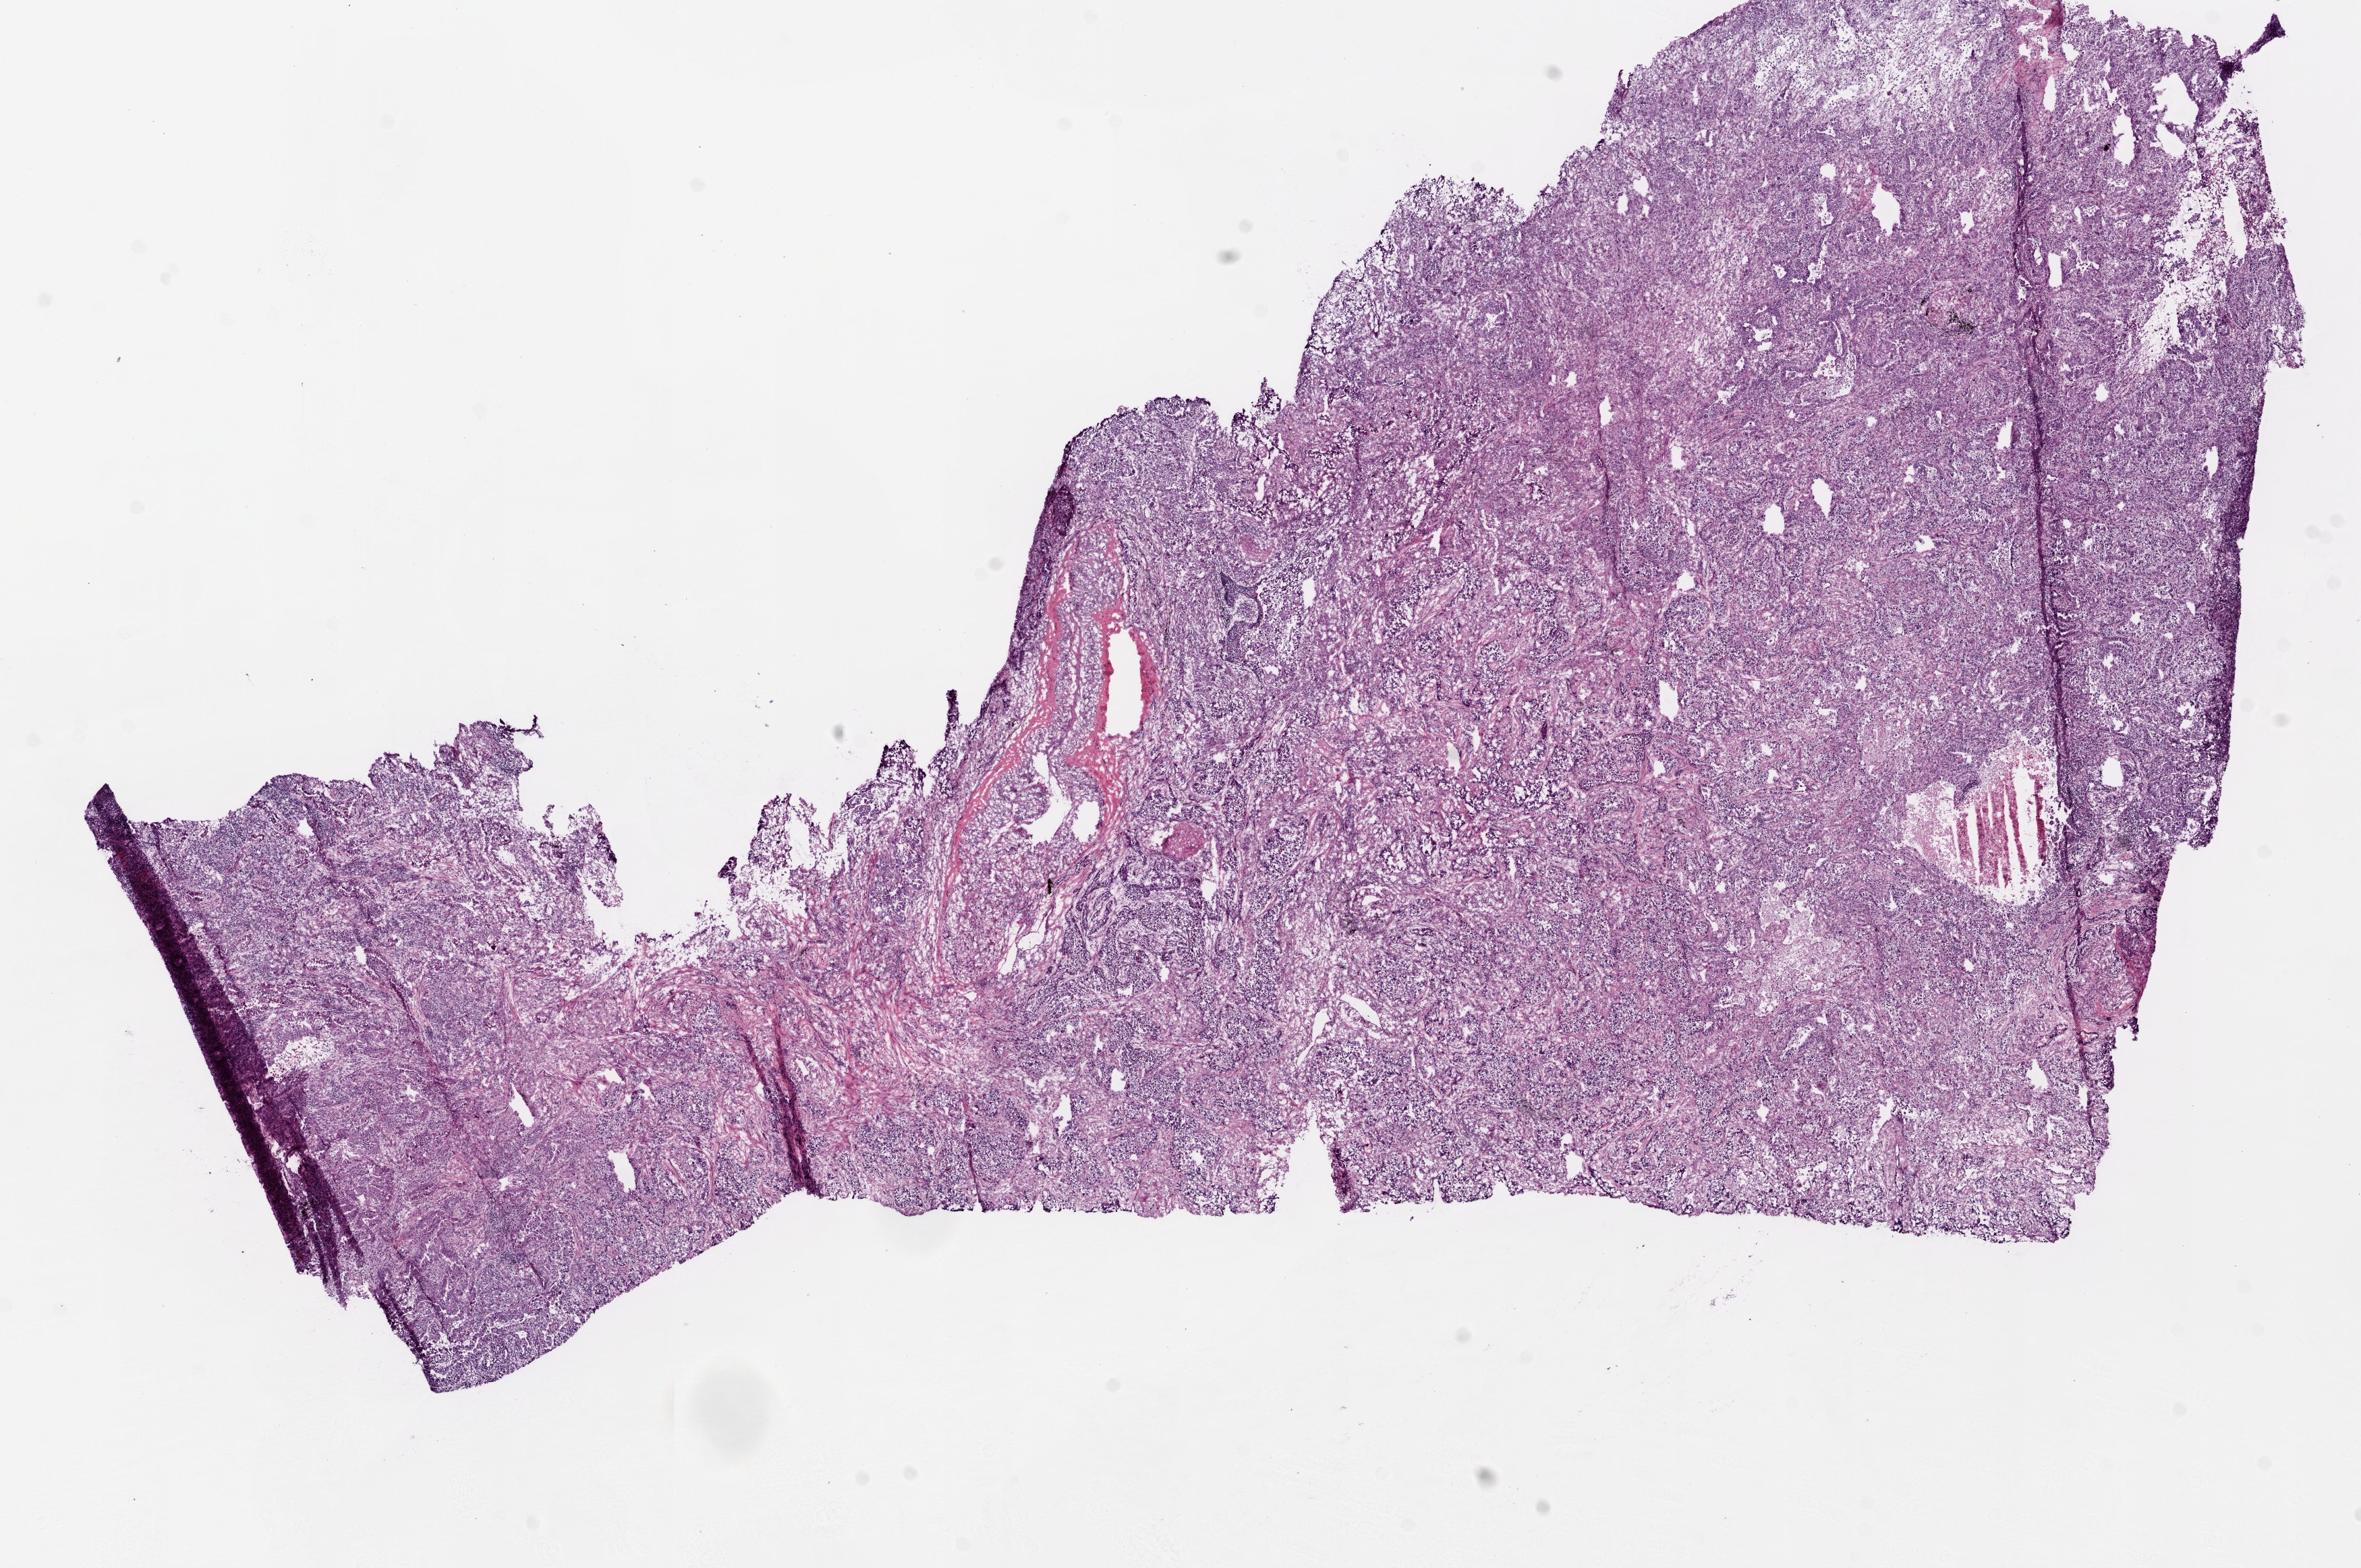
Whole-slide histology image, H&E, shown as a low-resolution overview of the whole scanned area (about 14.0 x 9.3 mm). Frozen section. Primary tumour sample from the lung. Female patient; age at initial diagnosis 56 years. Composition of this section per pathologist review: tumour nuclei 70%, normal cells 3%, stromal cells 15%, necrosis 5%.
Laterality: right. TNM: T2 NX M1. Histologic diagnosis: Adenocarcinoma with mixed subtypes (lower lobe, lung). AJCC pathologic stage: IV (6th edition).